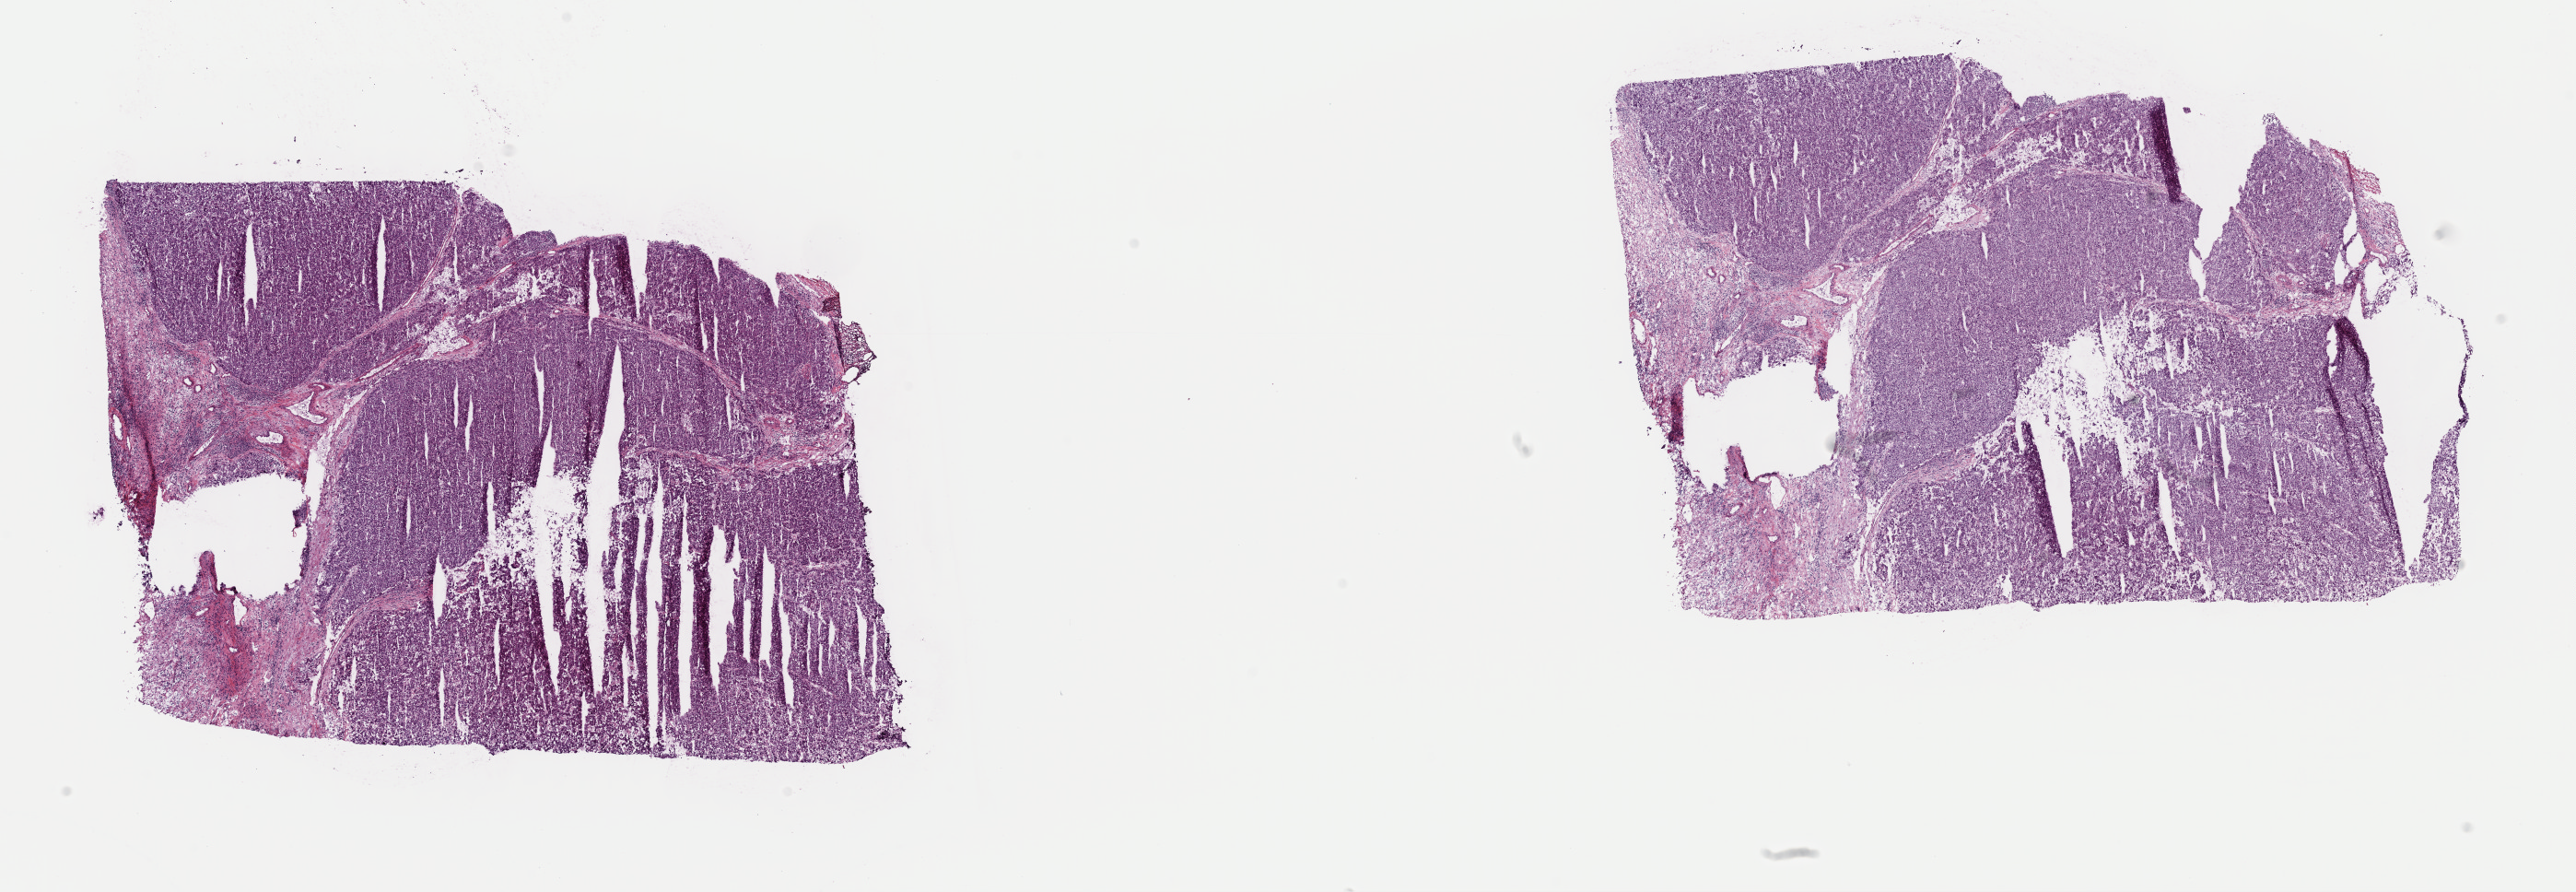
Whole-slide histology image, H&E, whole scanned area (about 22.1 x 7.6 mm) shown as a low-resolution overview. Frozen section. Liver, primary tumour sample. Female patient; age at initial diagnosis 77 years. Histologic grade: G1 (well differentiated). Composition of this section per pathologist review: tumour cells 73%, tumour nuclei 80%, normal cells 0%, stromal cells 20%, necrosis 7%. Inflammatory infiltration, as recorded: lymphocyte infiltration 12%, monocyte infiltration 1%, neutrophil infiltration 1%.
- AJCC pathologic stage: I (7th edition)
- pathologic diagnosis: Hepatocellular carcinoma, NOS